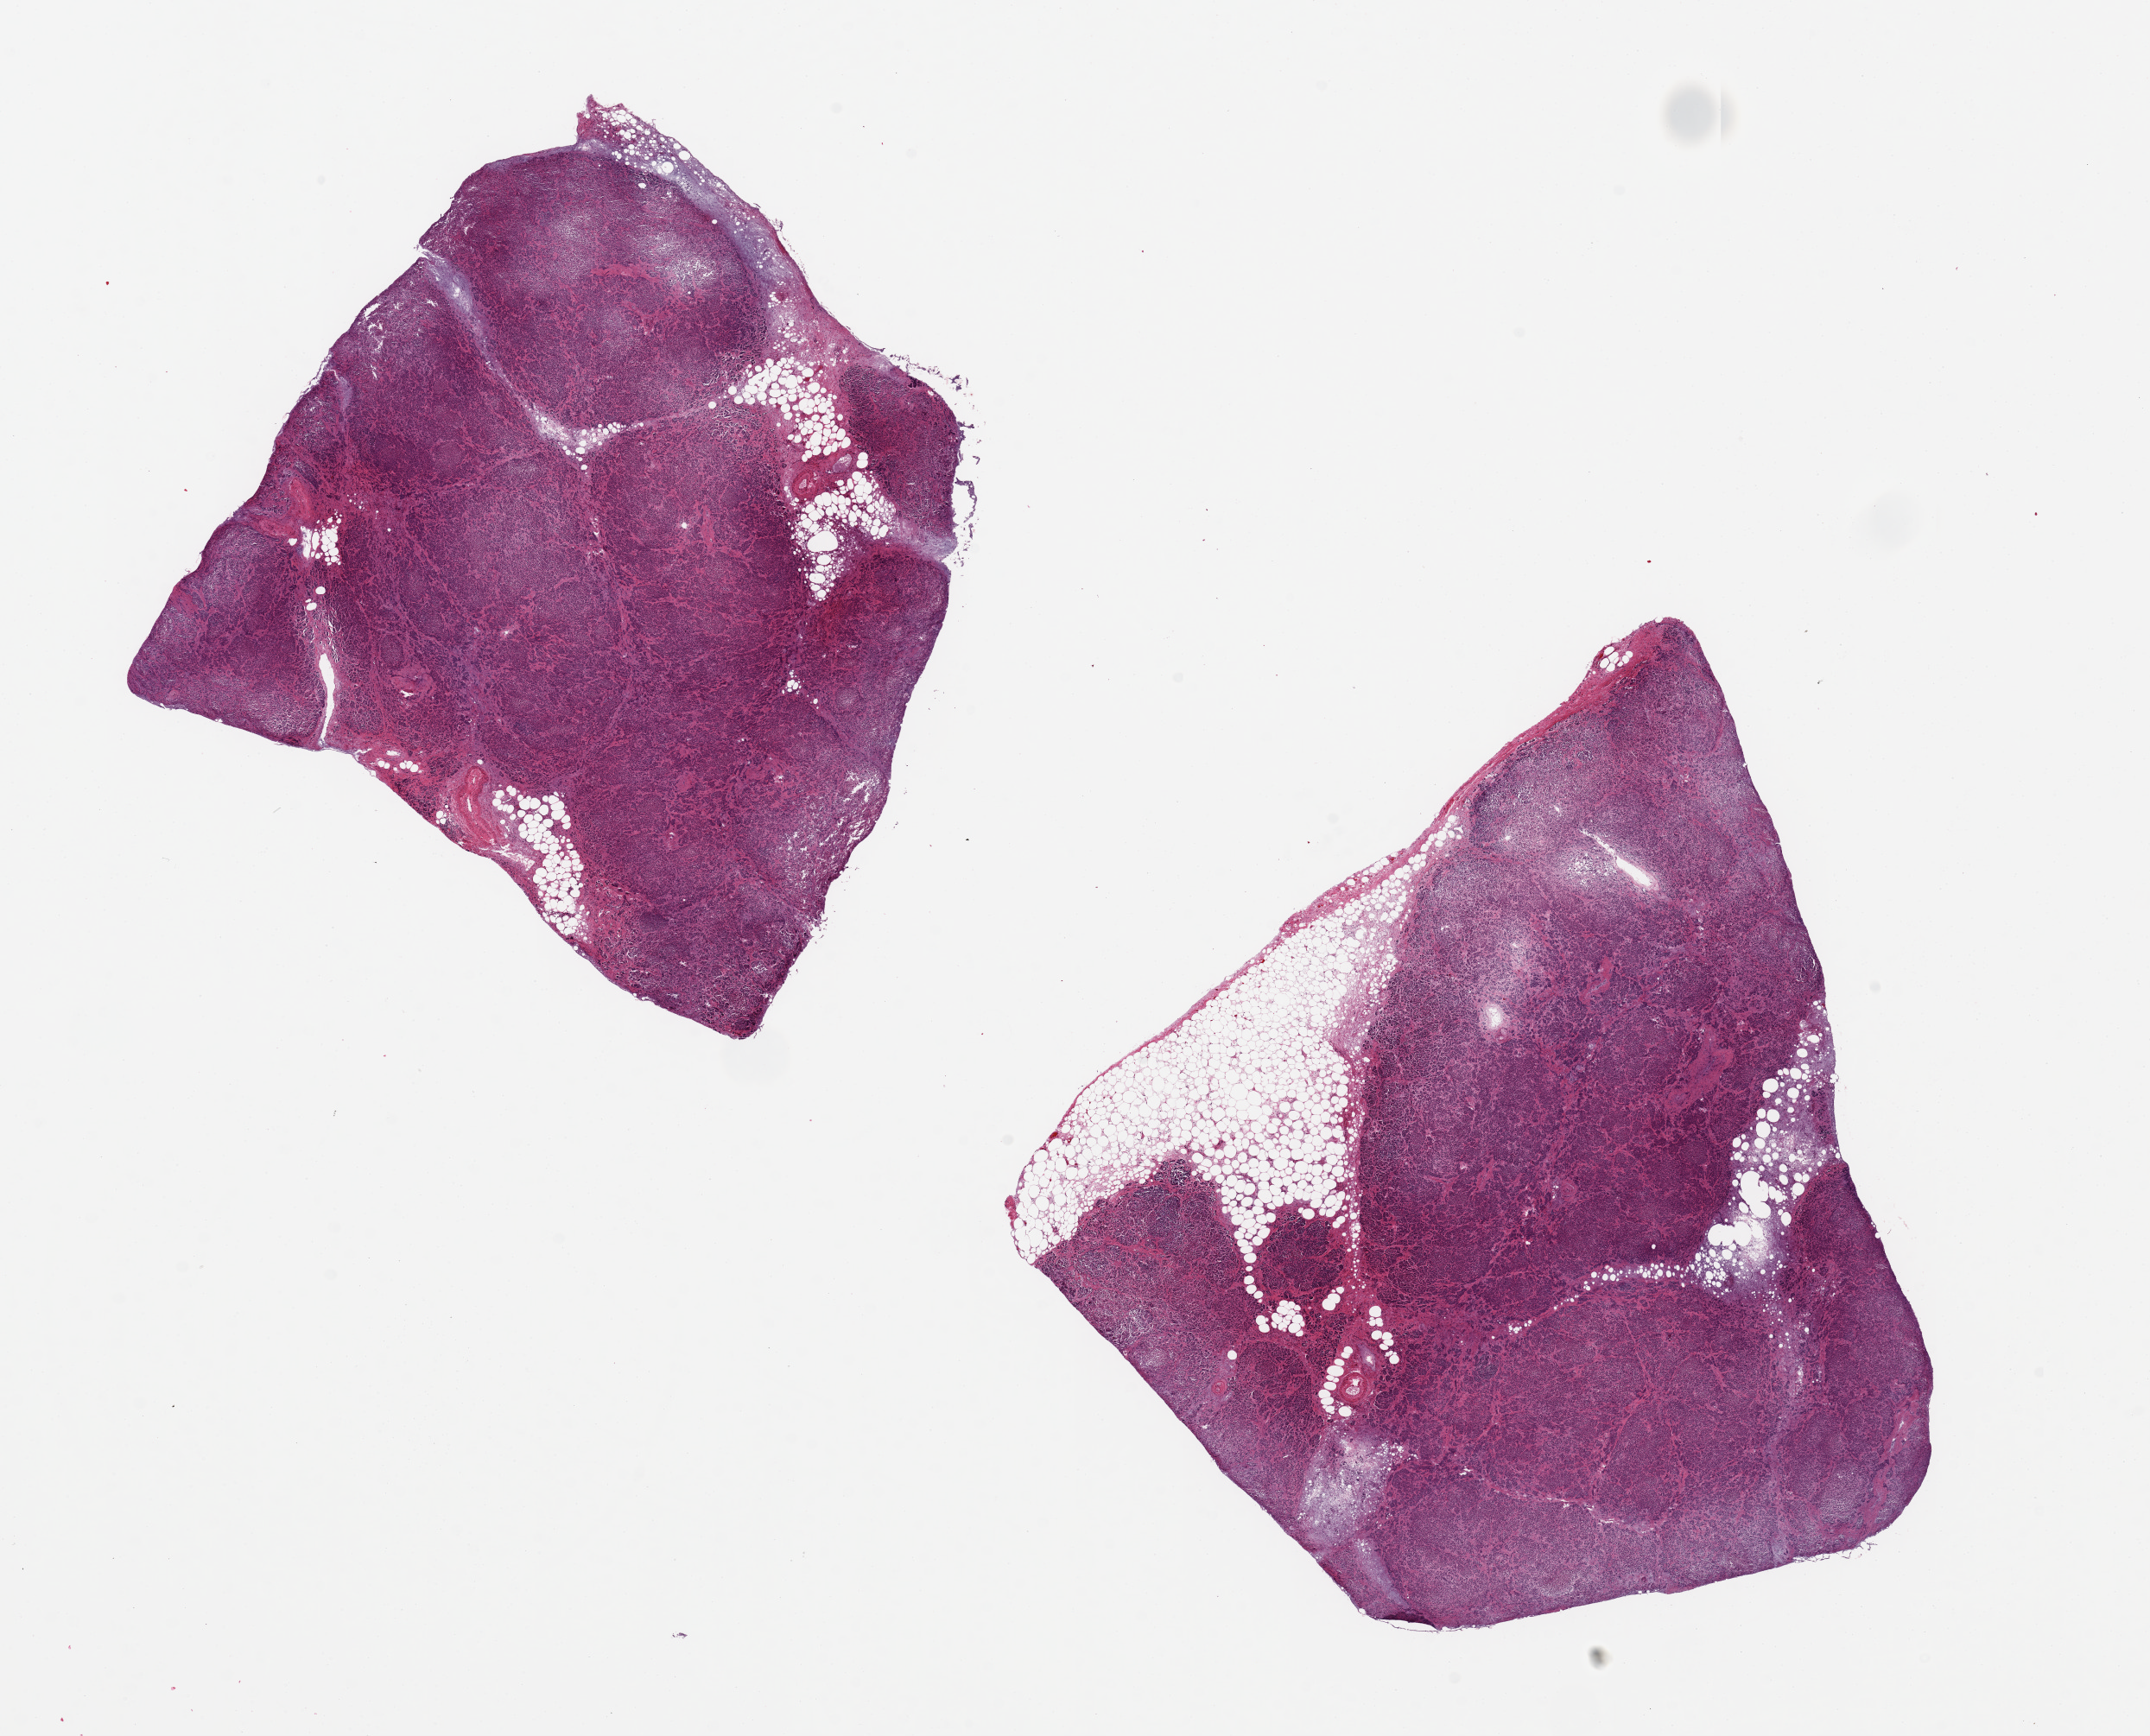
Digitized haematoxylin and eosin-stained section, shown as a low-resolution overview of the whole scanned area (about 19.7 x 15.9 mm); PAXgene-fixed, paraffin-embedded tissue; section of pancreas (target tissue); donor tissue sample. Donor: male.
Review note (as recorded): 2 pieces 8x8 & 6x6 mm; poor parenchymal preservation and saponification of adjacent fat (~10 and 20% of aliquots.